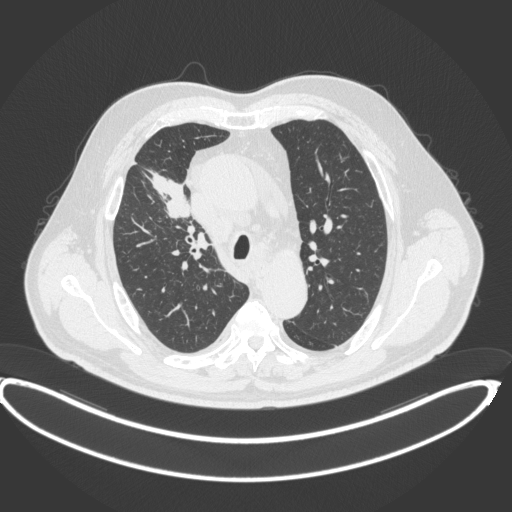
Chest CT, one axial slice. Slice 287 of 395 in the series (ordered by position). Reconstruction kernel B31f. 120 kVp. Lung window (W 1500 / L -600 HU). 512 × 512 image matrix. Patient: male, 62 years. Case-level facts recorded for this patient, not image findings: clinical TNM (as recorded): T1c N3 M1c.
Structures marked on this image (rectangle marked by the reading radiologist):
- lung tumour (recorded histology: adenocarcinoma): bounding box [x1, y1, x2, y2] px = [143, 167, 193, 220]